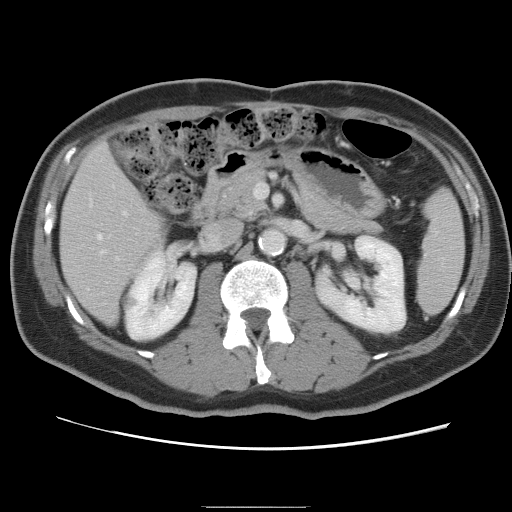
Contrast-enhanced abdominal CT, one axial slice. Slice 36 of 87 in the series (ordered by position). Intravenous contrast given. Soft-tissue window (W 400 / L 40 HU). 512 × 512 image matrix, field of view 363 × 363 mm. Male patient, age 63 years. From the clinical record (not read from this slice): diagnosis: colorectal cancer liver metastases, imaged before liver resection; multiple liver metastases: no.
Structures marked on this image (manually delineated by an expert):
- hepatic veins: bounding box <98,234,104,251> (left, top, right, bottom; pixels)
- liver: <61,143,163,323>
- planned liver remnant (the part of the liver to remain after resection): <61,143,163,323>
- portal vein (with intrahepatic branches): <115,209,128,261>